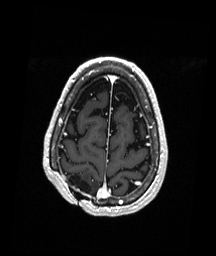
Brain MRI from a brain-tumour surgery series, one axial slice; position 50 of 192 along the scan axis; T1-weighted post-contrast; 216 × 256 image matrix, field of view 211 × 250 mm. Case-level facts recorded for this patient, not image findings: histopathology: Astrocytoma; WHO grade: 3; IDH mutation: yes.
Annotated regions visible in this slice (expert manual segmentation):
- previous resection cavity: bounding box <65,173,91,193> (left, top, right, bottom; pixels)